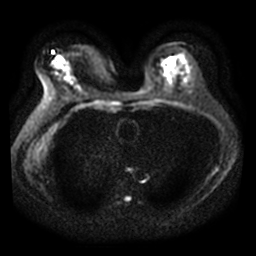
Breast MRI, one axial slice; diffusion-weighted series; image 2 of 4 stored at this slice position (different b-values; order by instance number); 3 T; 256 × 256 image matrix. Female patient.
Annotated regions visible in this slice (expert manual segmentation):
- tumour on diffusion-weighted imaging: box from (x=58, y=56) to (x=62, y=59) px